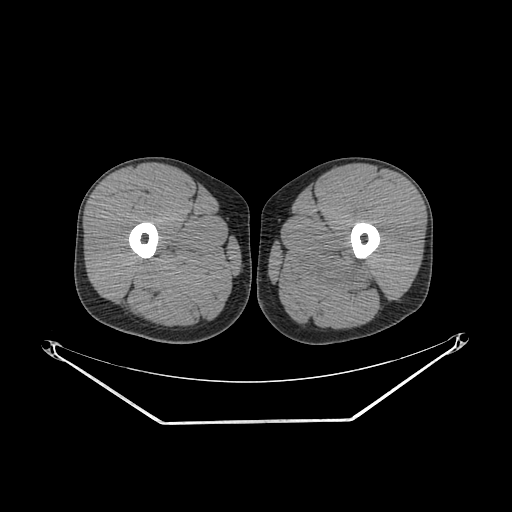
CT of an extremity soft-tissue mass (from a PET/CT study), one axial slice; slice 241 of 267 in the series (ordered by position); reconstruction kernel SOFT; 140 kVp; soft-tissue window (W 400 / L 40 HU); 3.75 mm slice thickness; 512 × 512 image matrix, field of view 500 × 500 mm. Male patient. Case-level facts recorded for this patient, not image findings: histological type: extraskeletal osteosarcoma; grade: high; site of the primary tumour: left adductur.
Outlined on this slice (expert contour drawn on MRI and transferred to this co-registered scan by the dataset authors):
- gross tumour volume (mass): bounding box [x1, y1, x2, y2] px = [283, 247, 380, 298]